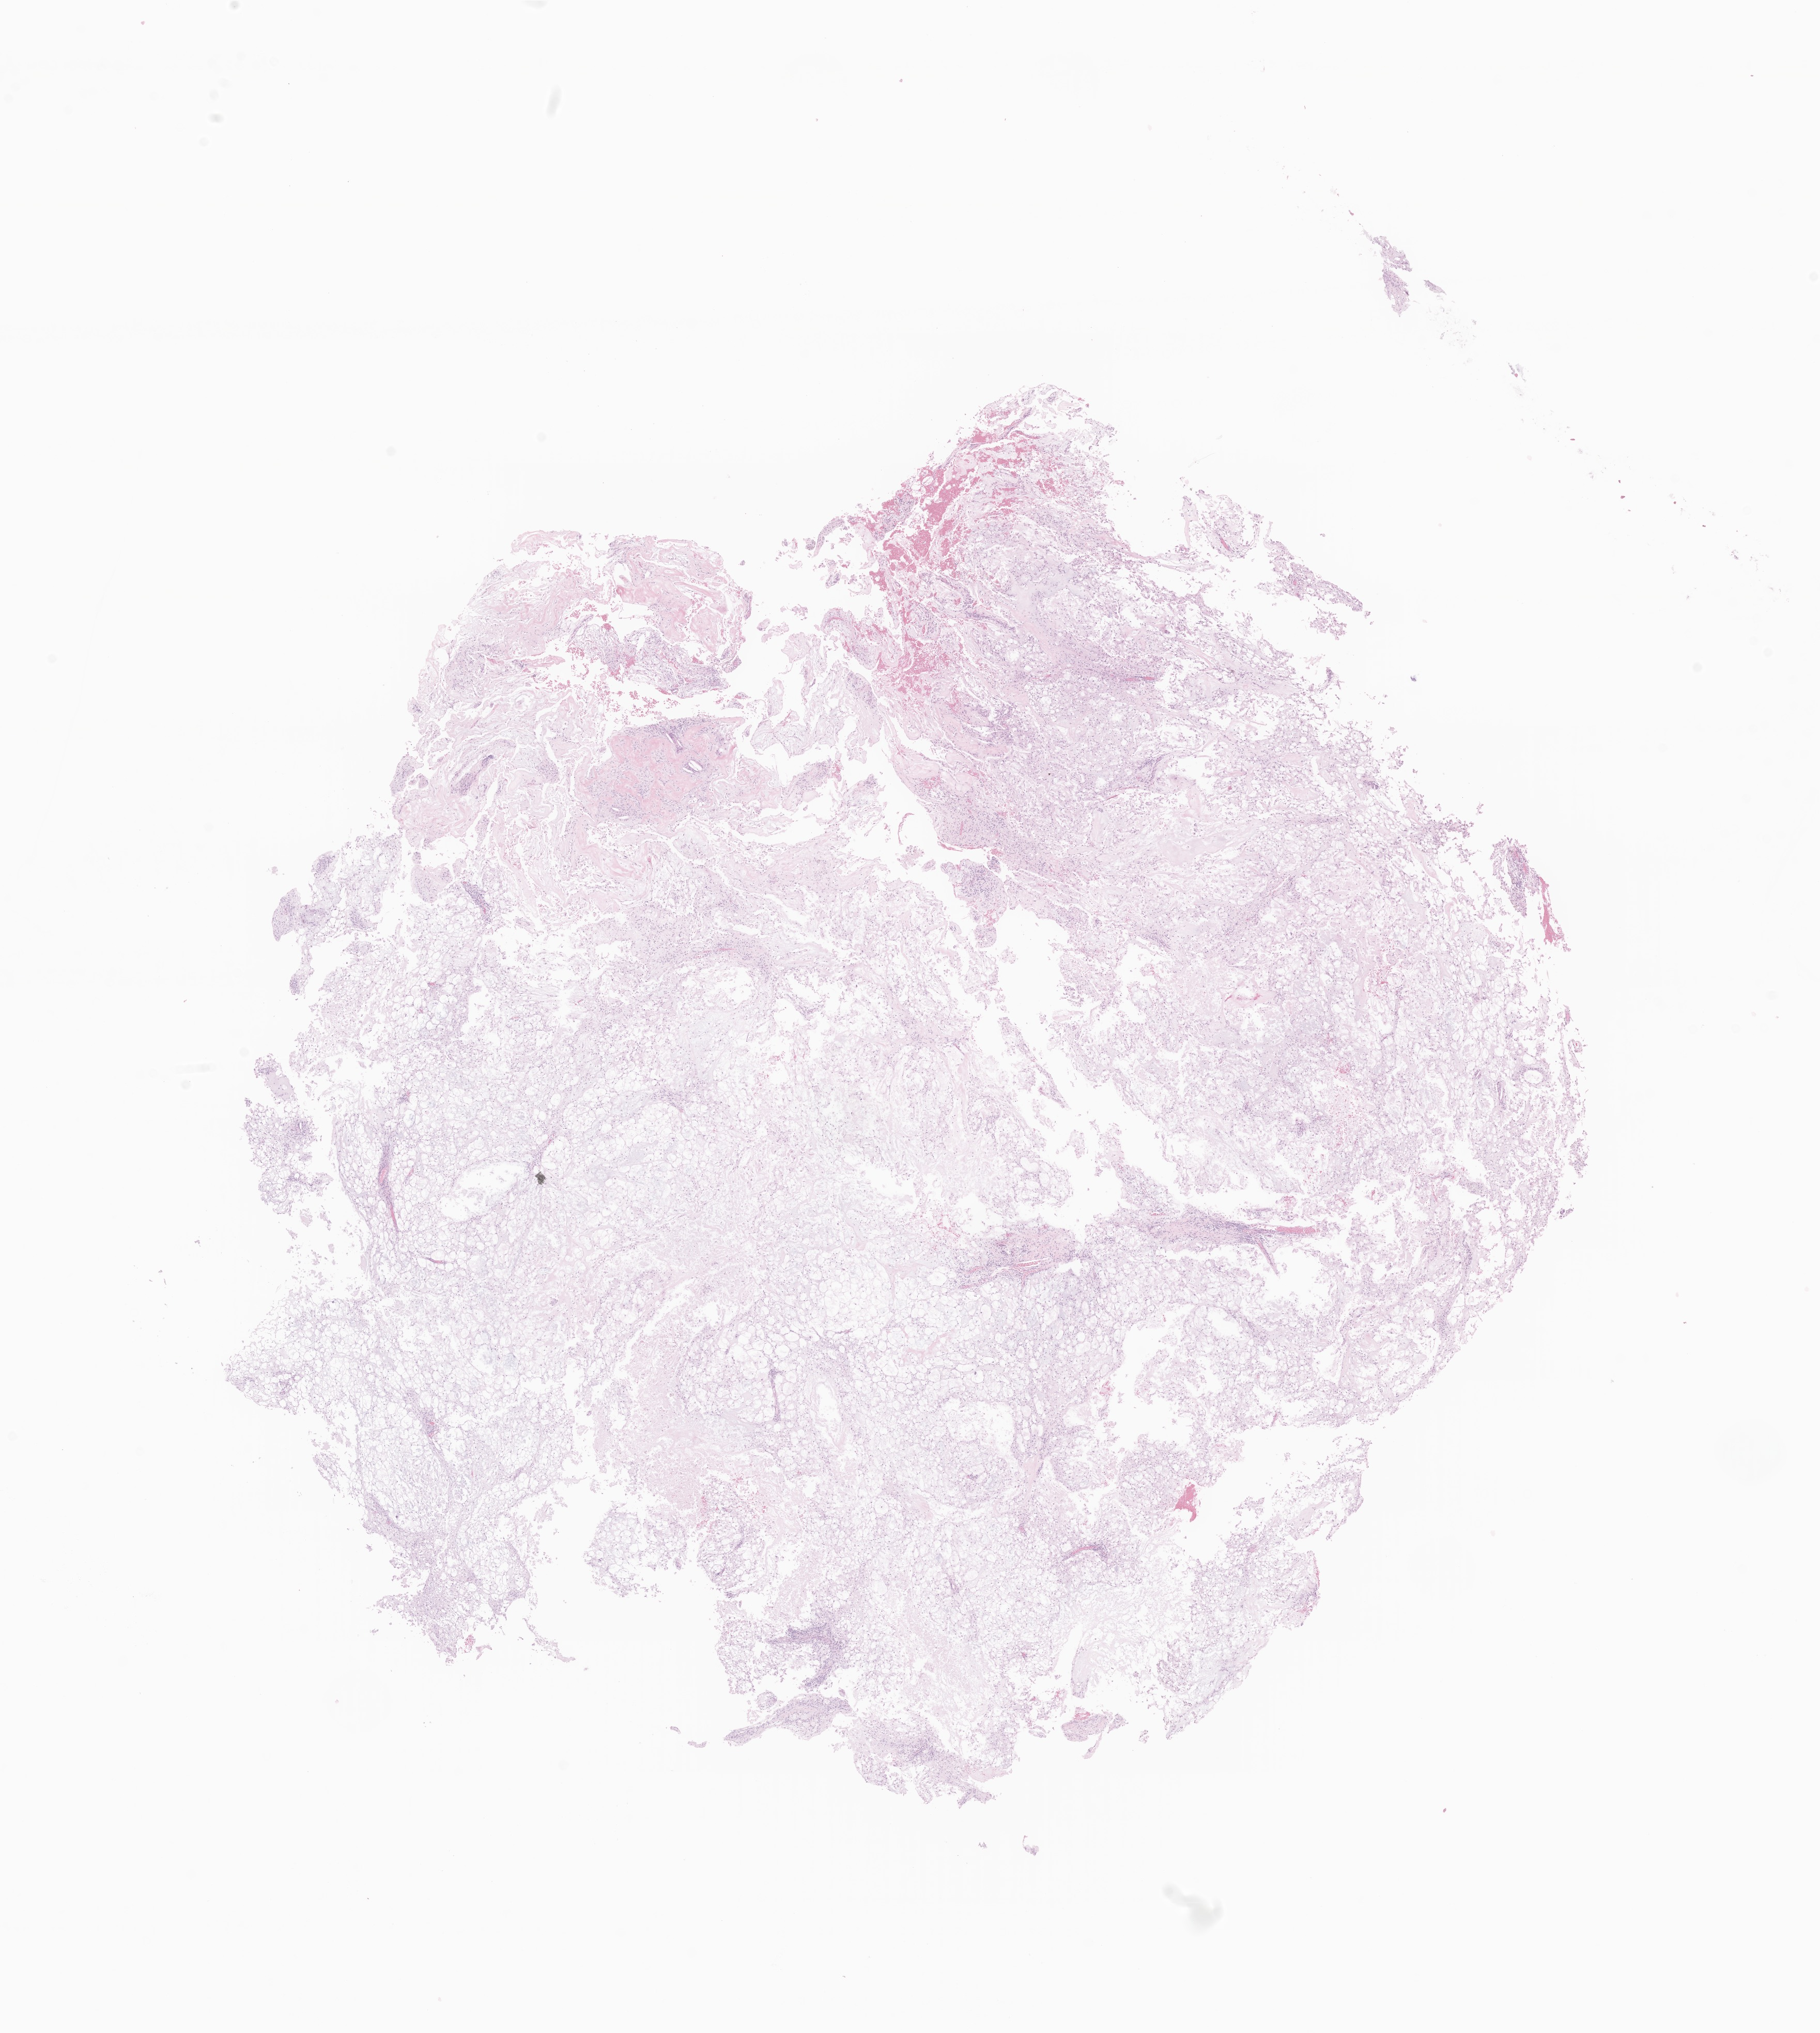
Whole-slide image, H&E stain of tumor tissue from the cranial and/or facial bone, shown as a low-resolution overview of the whole scanned area (about 14.8 x 16.6 mm), formalin-fixed paraffin-embedded section. Patient male; age 143 months (11 years 11 months).
Diagnosis: Chordoma, NOS.